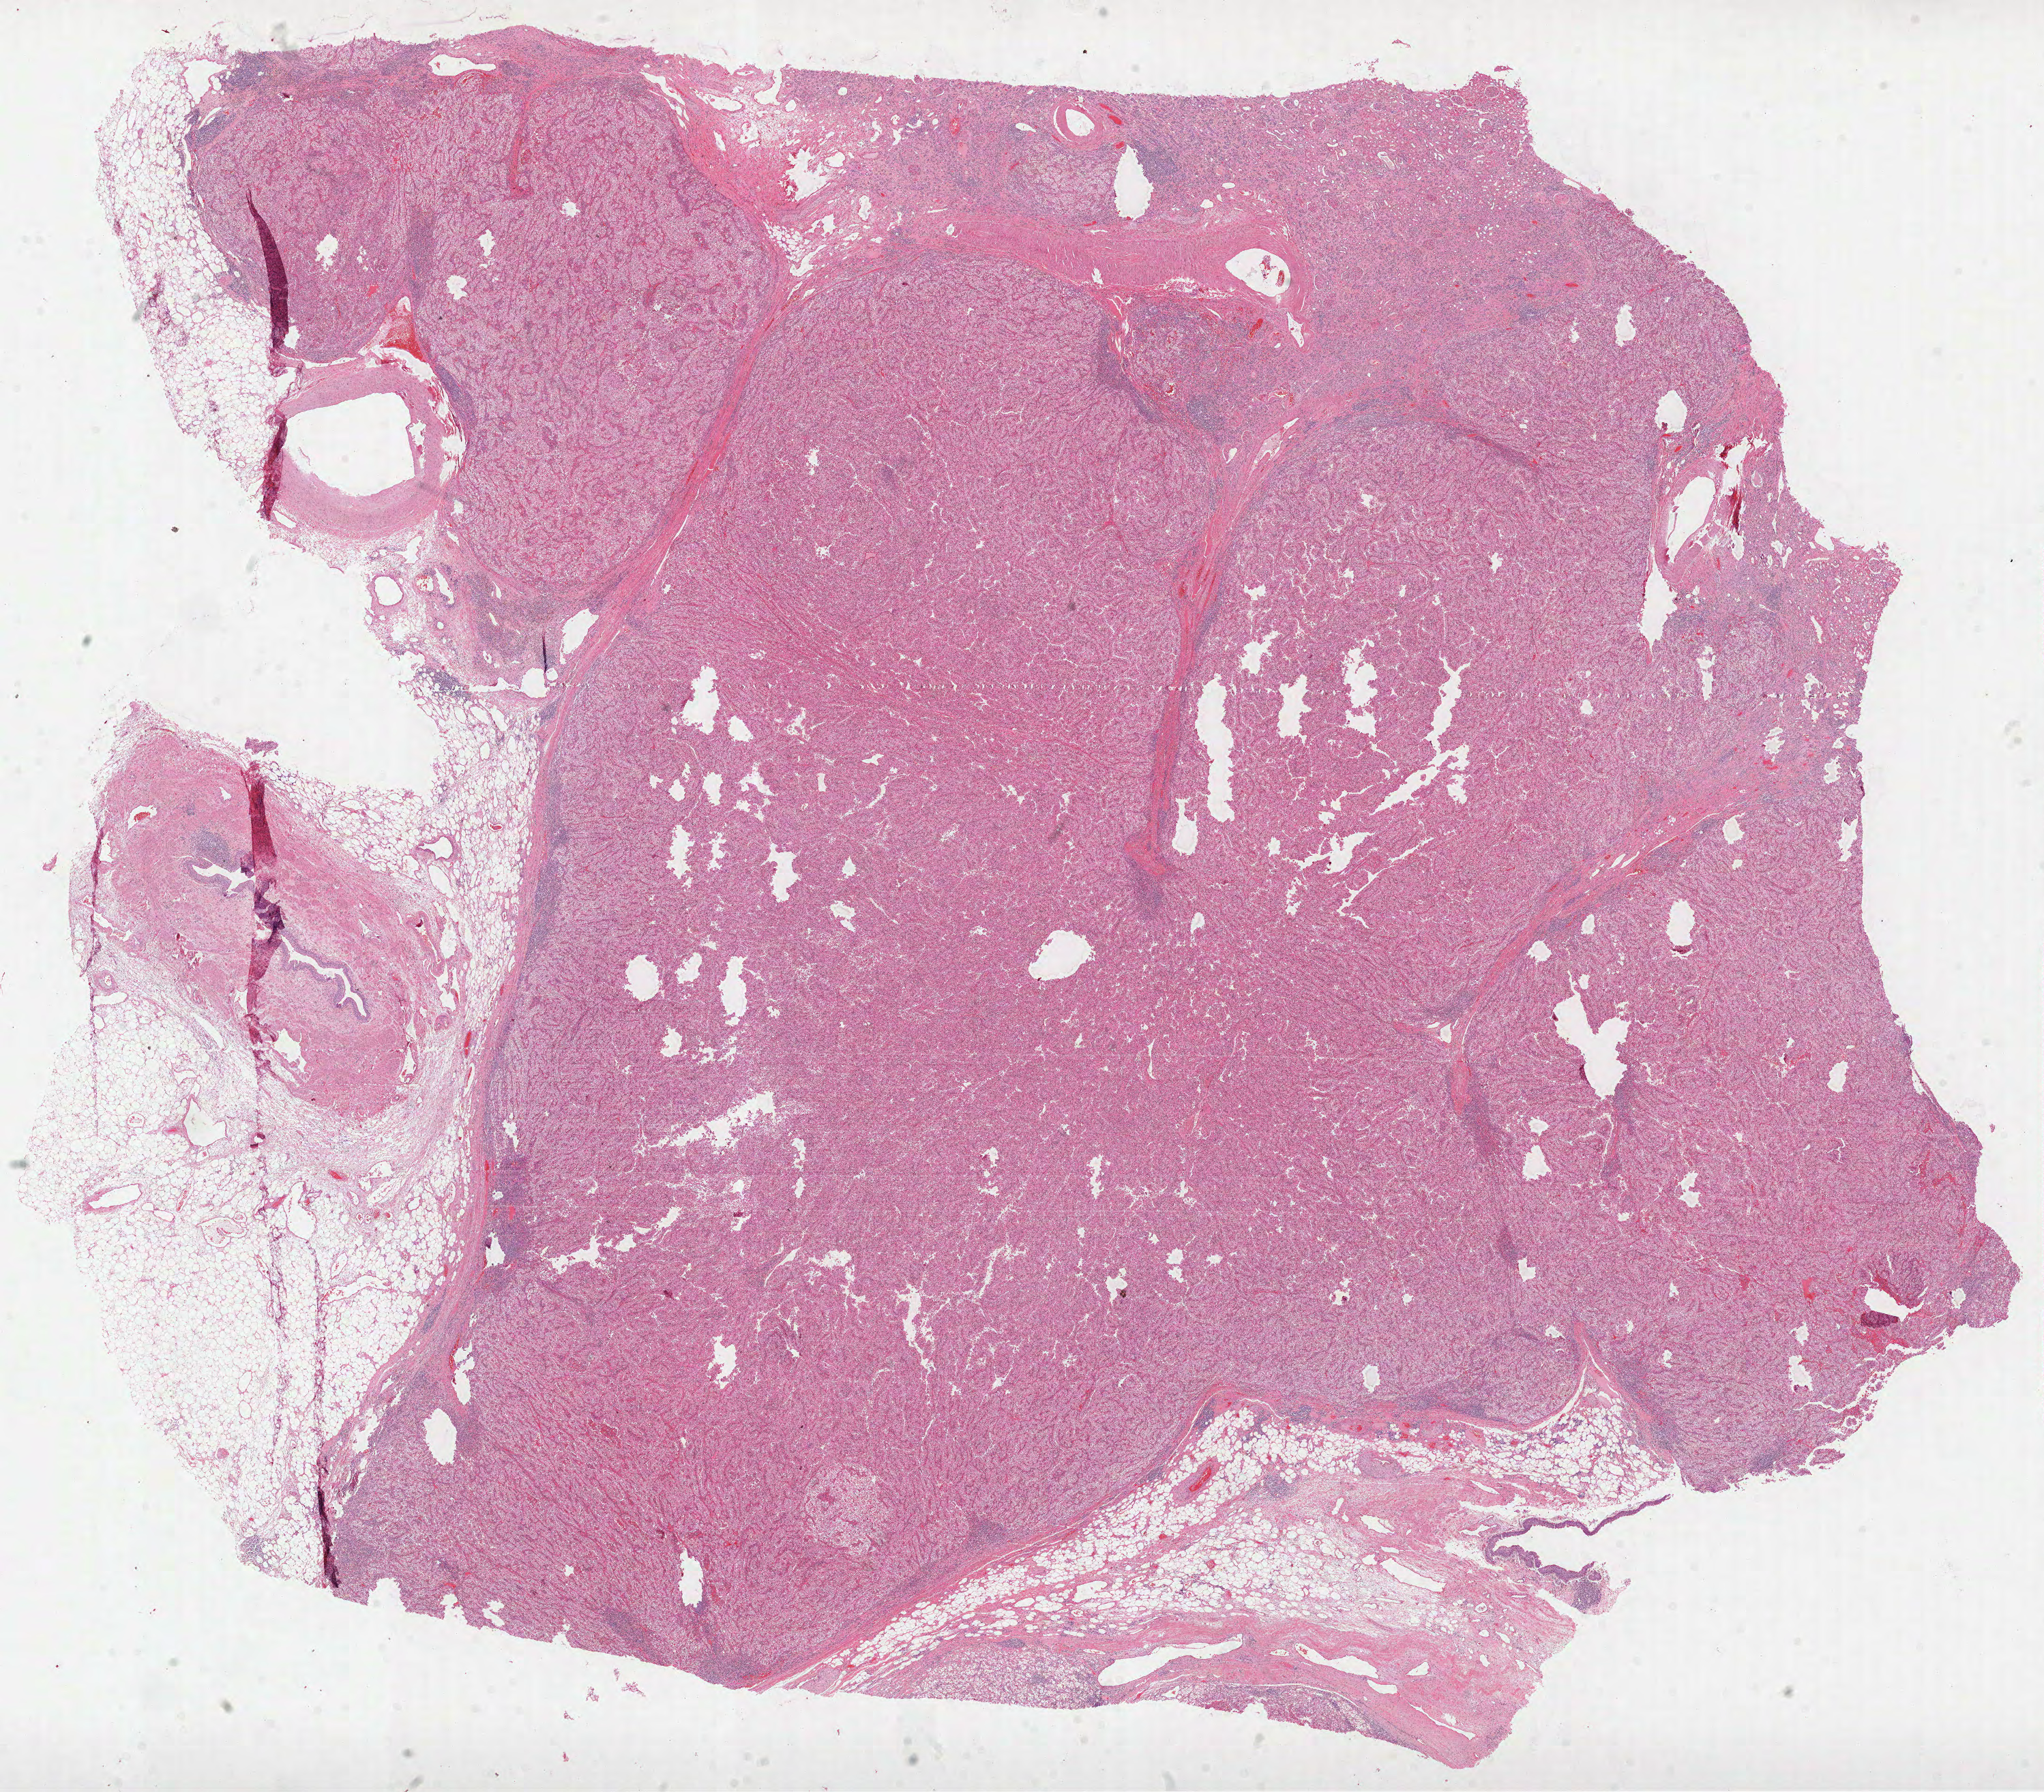
Hematoxylin and eosin (H&E) stained whole-slide image, low-resolution overview of the scanned area, about 24.2 x 21.2 mm; formalin-fixed paraffin-embedded (FFPE) diagnostic section; kidney, primary tumour sample. Male, age 81 years at initial diagnosis. Histologic grade: G3 (poorly differentiated).
- pathologic diagnosis: Clear cell adenocarcinoma, NOS
- AJCC pathologic stage: III